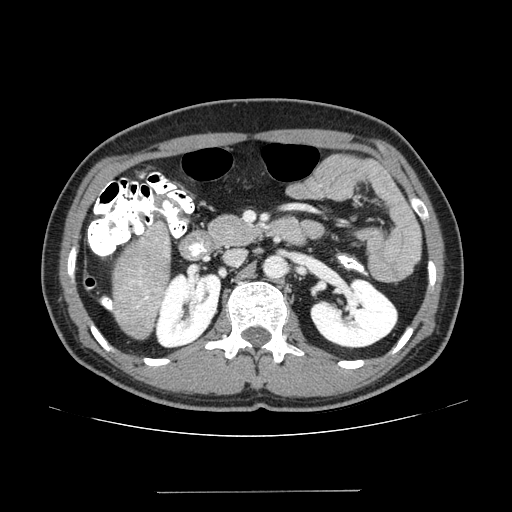
Contrast-enhanced abdominal CT (liver protocol), one axial slice. Slice 60 of 131 in the series (ordered by position). One of 2 acquisitions stored at this slice position. Soft-tissue window (W 400 / L 40 HU). 2.5 mm slice thickness. 512 × 512 image matrix, field of view 380 × 380 mm. Case-level facts recorded for this patient, not image findings: diagnosis: hepatocellular carcinoma (patient treated with transarterial chemoembolisation; whether this scan precedes or follows treatment is not stated here); TNM stage (as recorded): Stage-I; Child-Pugh class: A; tumour differentiation: poorly differentiated; tumour nodularity: uninodular.
Outlined on this slice (semi-automatic segmentation, software-assisted and operator-edited):
- liver parenchyma outside the tumour (the mass and vessels are separate outlines, so this box may not span the whole liver): bounding box [x1, y1, x2, y2] px = [112, 222, 170, 336]
- liver vessels: [145, 296, 148, 299]